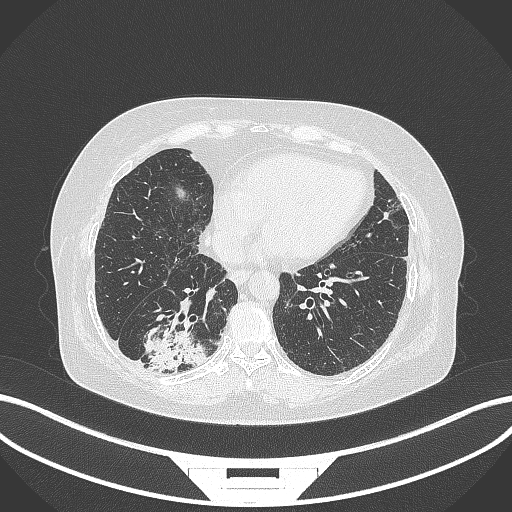
Chest CT, one axial slice; slice 74 of 296 in the series (ordered by position); reconstruction kernel B70f; 120 kVp; lung window (W 1500 / L -600 HU); 512 × 512 image matrix. Patient: female, 65 years. From the clinical record (not read from this slice): clinical TNM (as recorded): T2b N1 M0; histopathological grade: G1.
Annotated regions visible in this slice (bounding box drawn by a radiologist):
- lung tumour (recorded histology: adenocarcinoma): bounding box <141,324,206,374> (left, top, right, bottom; pixels)